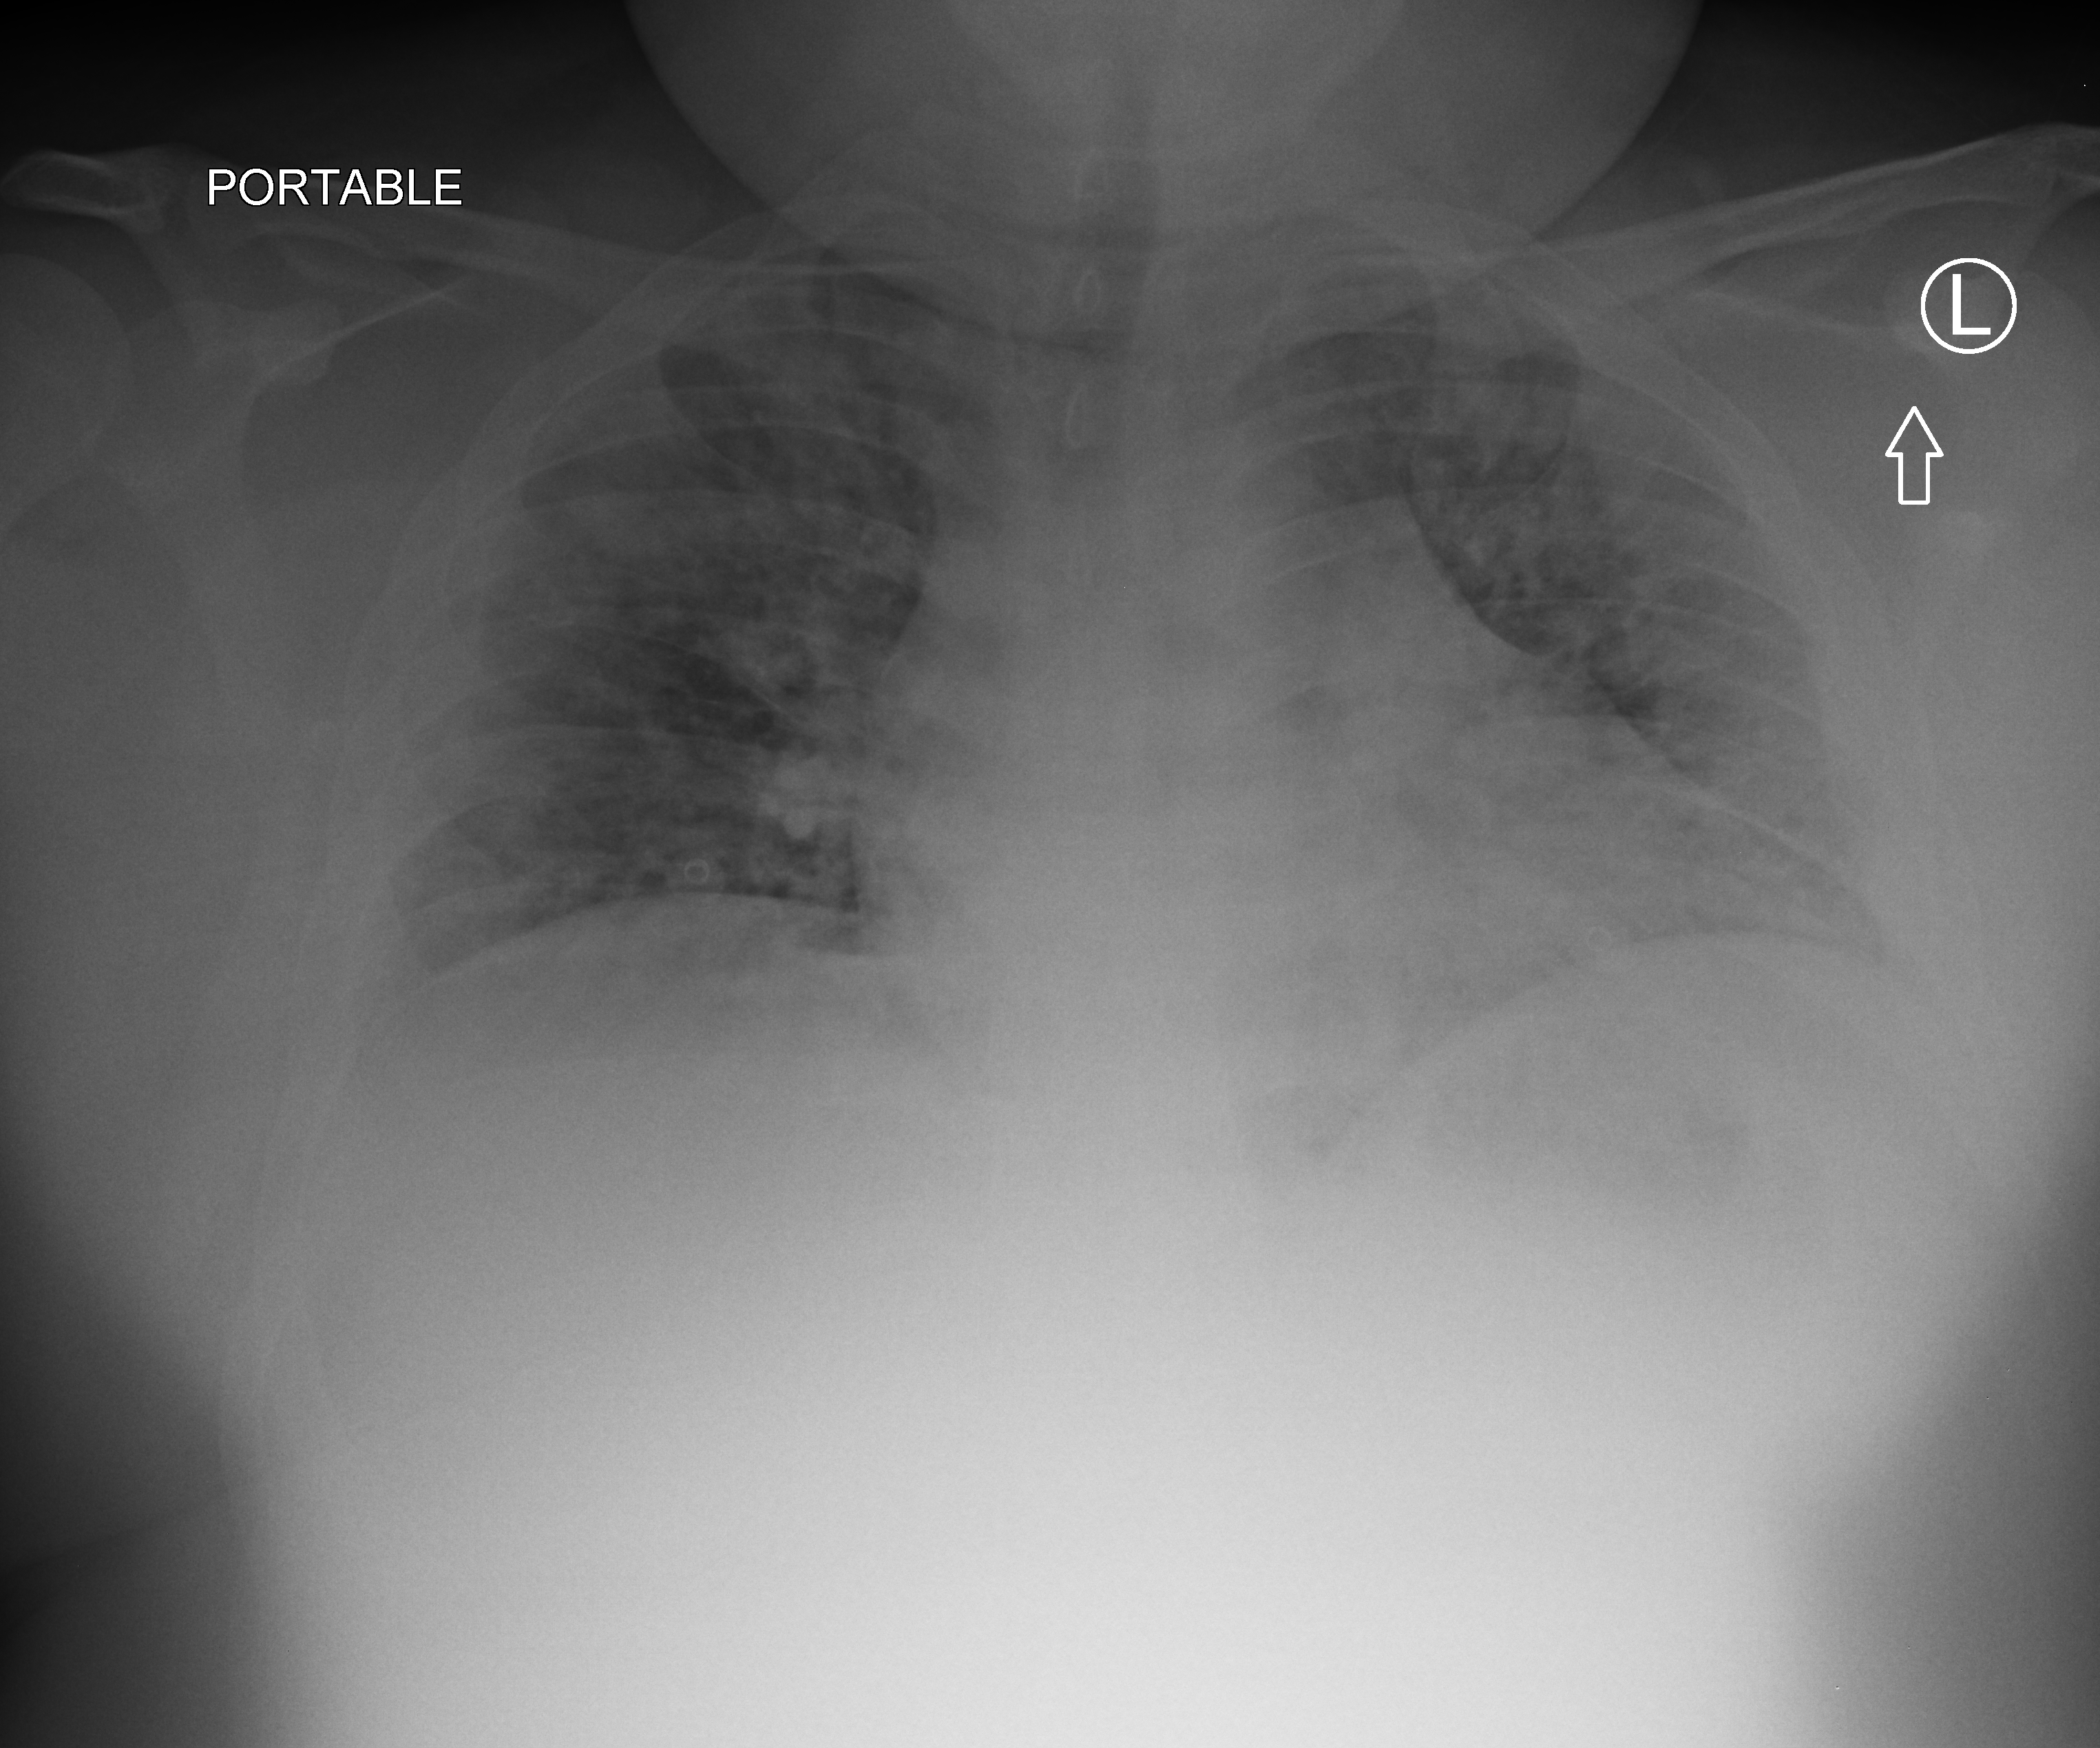
Chest X-ray (portable); anteroposterior (AP) projection. Male patient hospitalised with COVID-19, age 18–59 years.
From the hospital-stay record, not from the radiograph (when in the stay this image was taken is not recorded): length of hospital stay: 12 days; admitted to intensive care during this hospital stay: no; diabetes (admission record): yes.